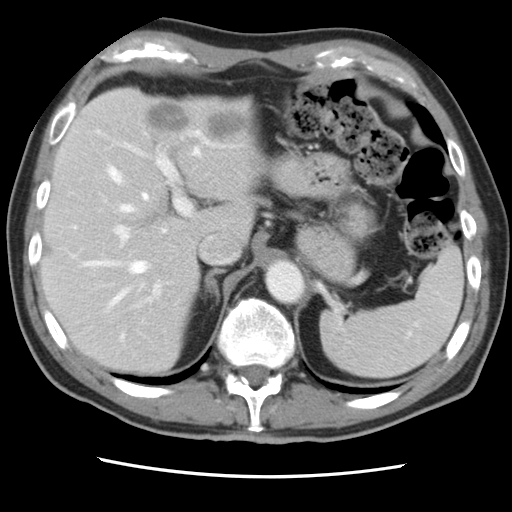
Contrast-enhanced abdominal CT, one axial slice. Position 59 of 83 along the scan axis. Intravenous contrast given. Soft-tissue window (W 400 / L 40 HU). 5 mm slice thickness. 512 × 512 image matrix. Male patient, age 69 years. From the clinical record (not read from this slice): diagnosis: colorectal cancer liver metastases, imaged before liver resection; multiple liver metastases: yes; largest metastasis: 3.5 cm.
Annotated regions visible in this slice (manually delineated by an expert):
- hepatic veins: bounding box <75,148,200,339> (left, top, right, bottom; pixels)
- liver: <42,88,256,374>
- planned liver remnant (the part of the liver to remain after resection): <43,143,208,373>
- portal vein (with intrahepatic branches): <113,129,242,302>
- liver metastasis: <149,104,190,131>
- liver metastasis: <207,109,249,139>